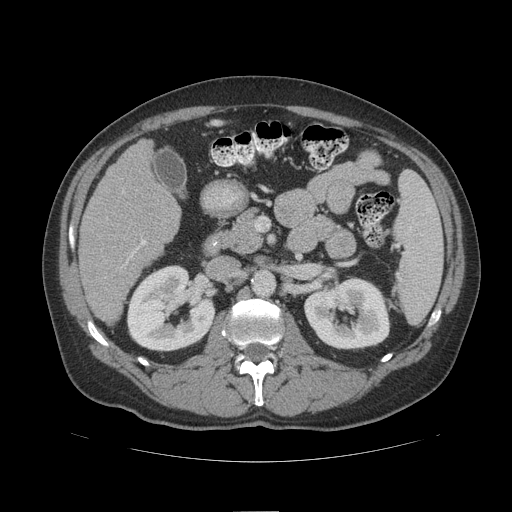
Contrast-enhanced abdominal CT (liver protocol), one axial slice; slice 49 of 109 in the series (ordered by position); reconstruction kernel STANDARD; soft-tissue window (W 400 / L 40 HU); 2.5 mm slice thickness; 512 × 512 image matrix. From the clinical record (not read from this slice): diagnosis: hepatocellular carcinoma (patient treated with transarterial chemoembolisation; whether this scan precedes or follows treatment is not stated here); TNM stage (as recorded): Stage-IIIB; Child-Pugh class: A; tumour differentiation: poorly differentiated; tumour nodularity: multinodular.
Annotated regions visible in this slice (semi-automatic segmentation, software-assisted and operator-edited):
- liver parenchyma outside the tumour (the mass and vessels are separate outlines, so this box may not span the whole liver): bounding box [x1, y1, x2, y2] px = [78, 140, 180, 324]
- liver vessels: [127, 240, 146, 262]